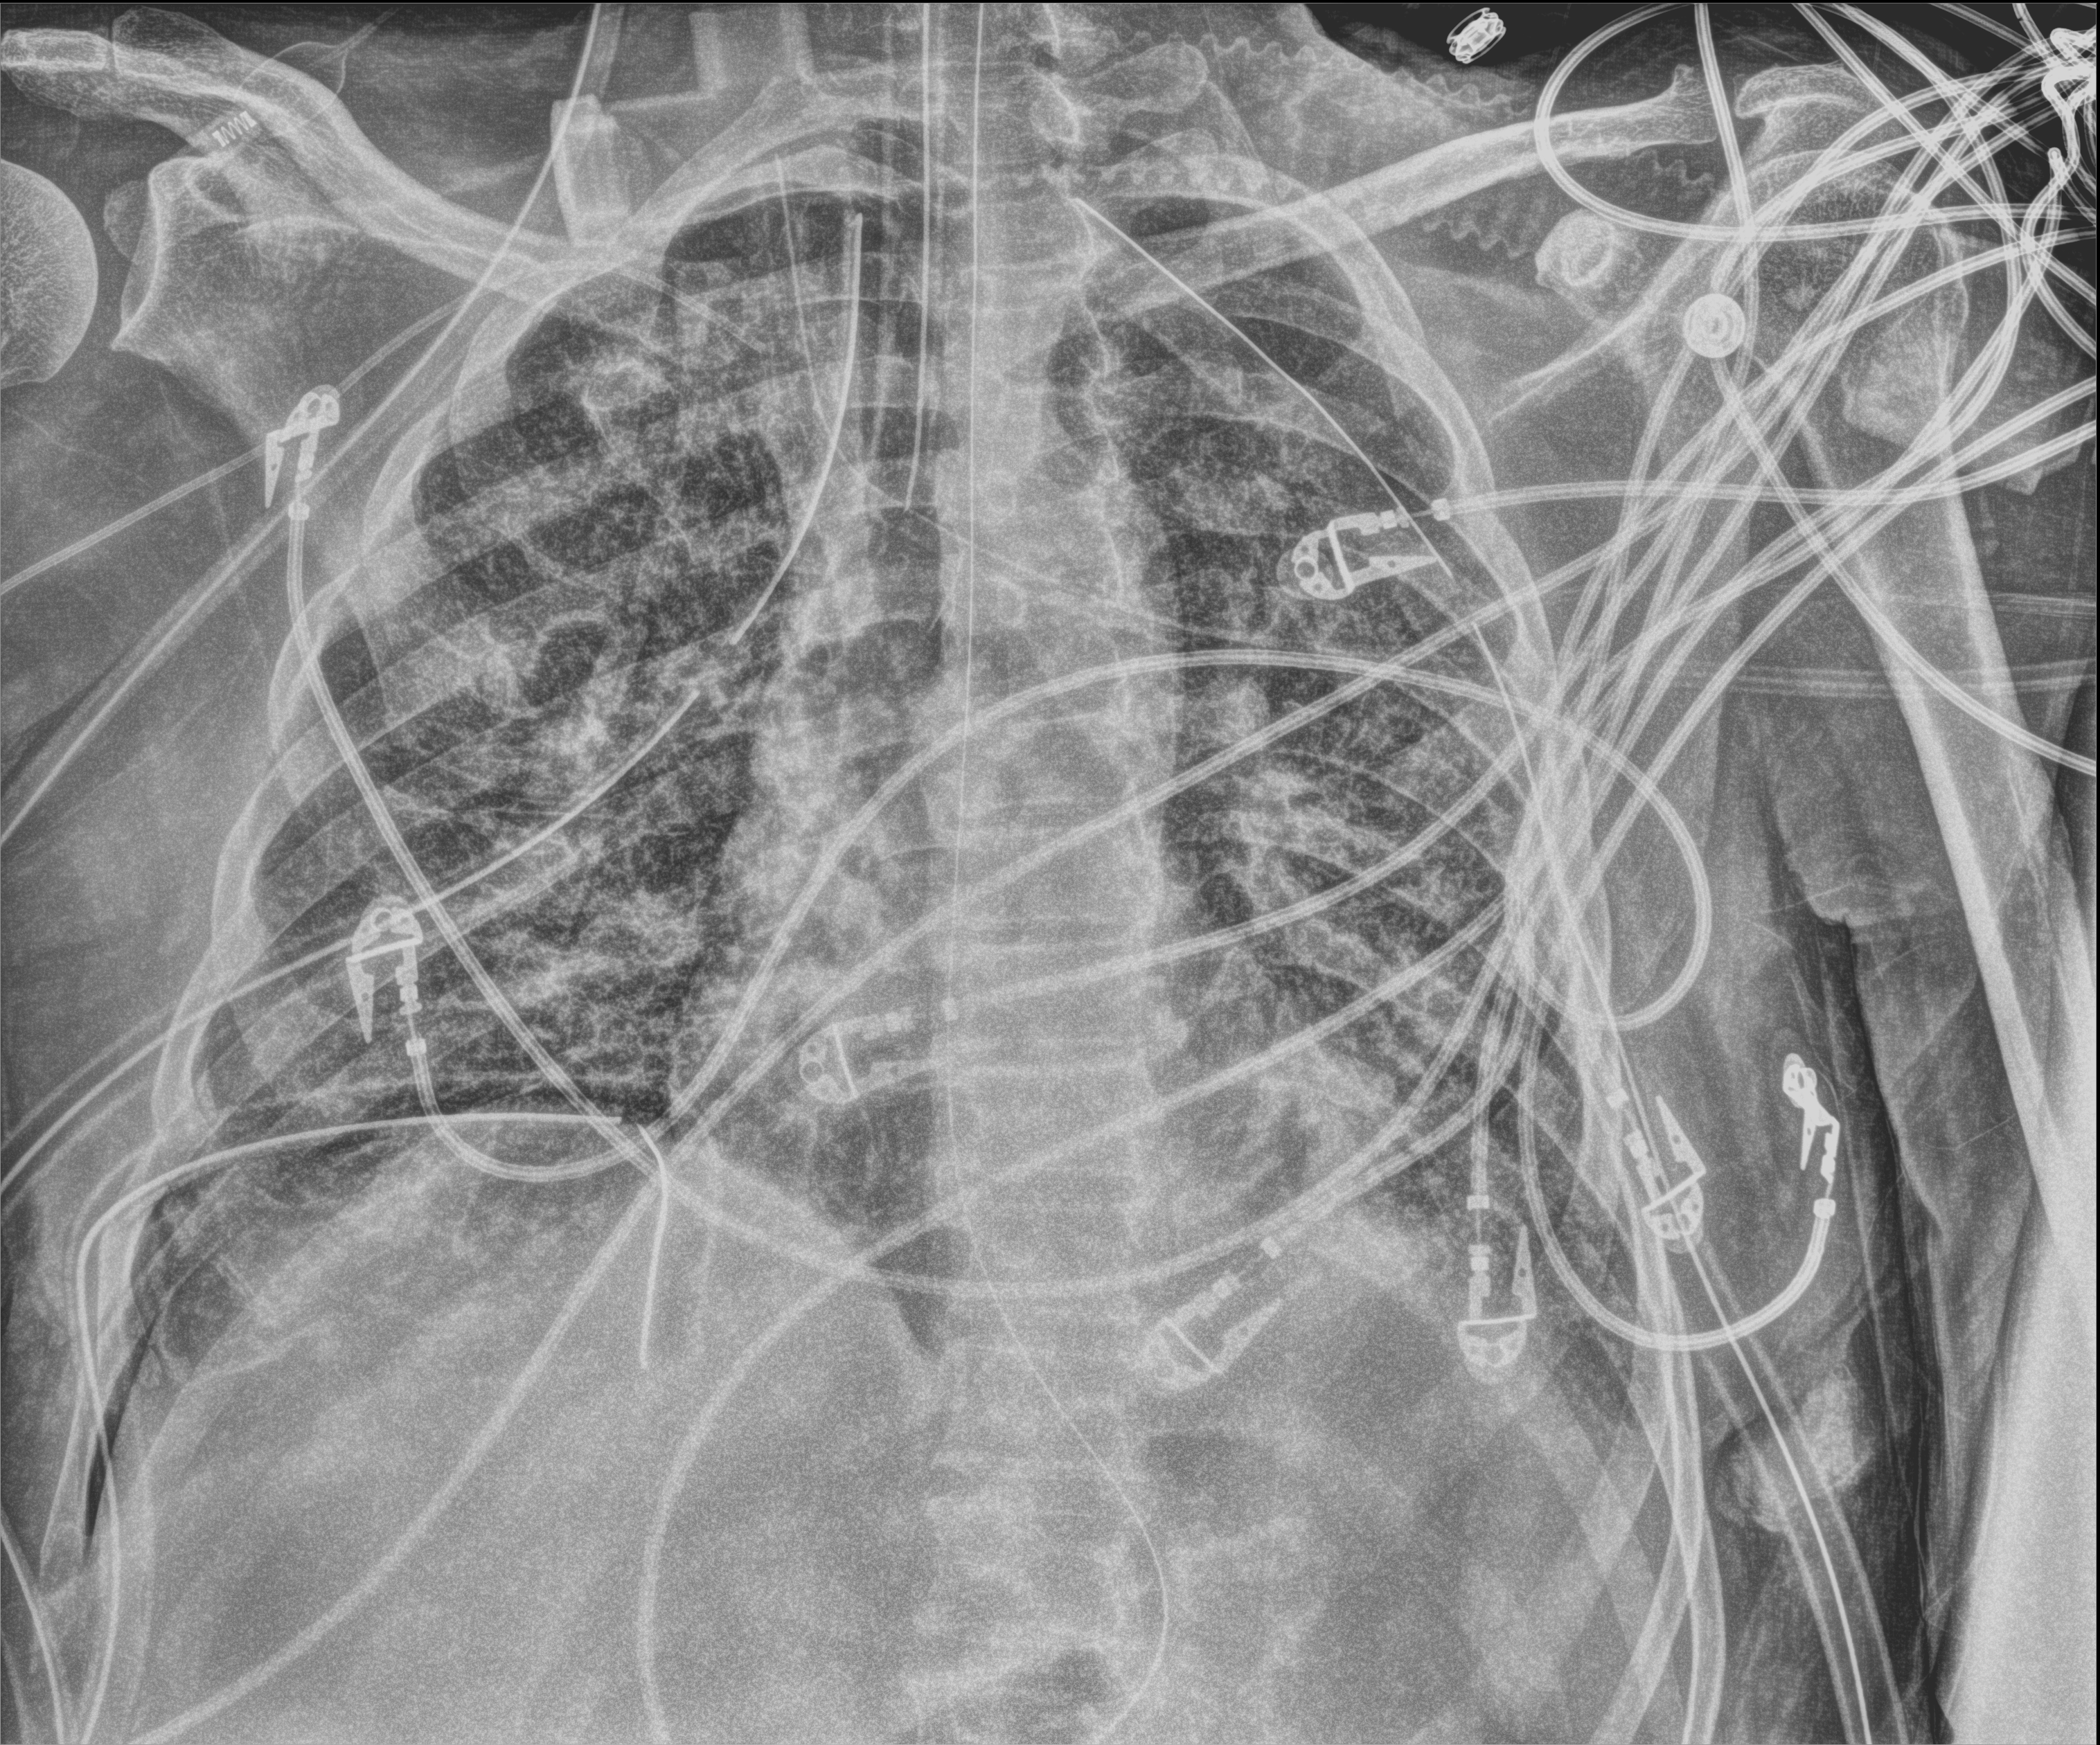
Chest X-ray (portable); anteroposterior (AP) projection. Patient hospitalised with COVID-19; male, aged 18–59 years.
Hospital-stay facts (about this admission, not read from this image; timing relative to this image not recorded):
- COPD (admission record): no